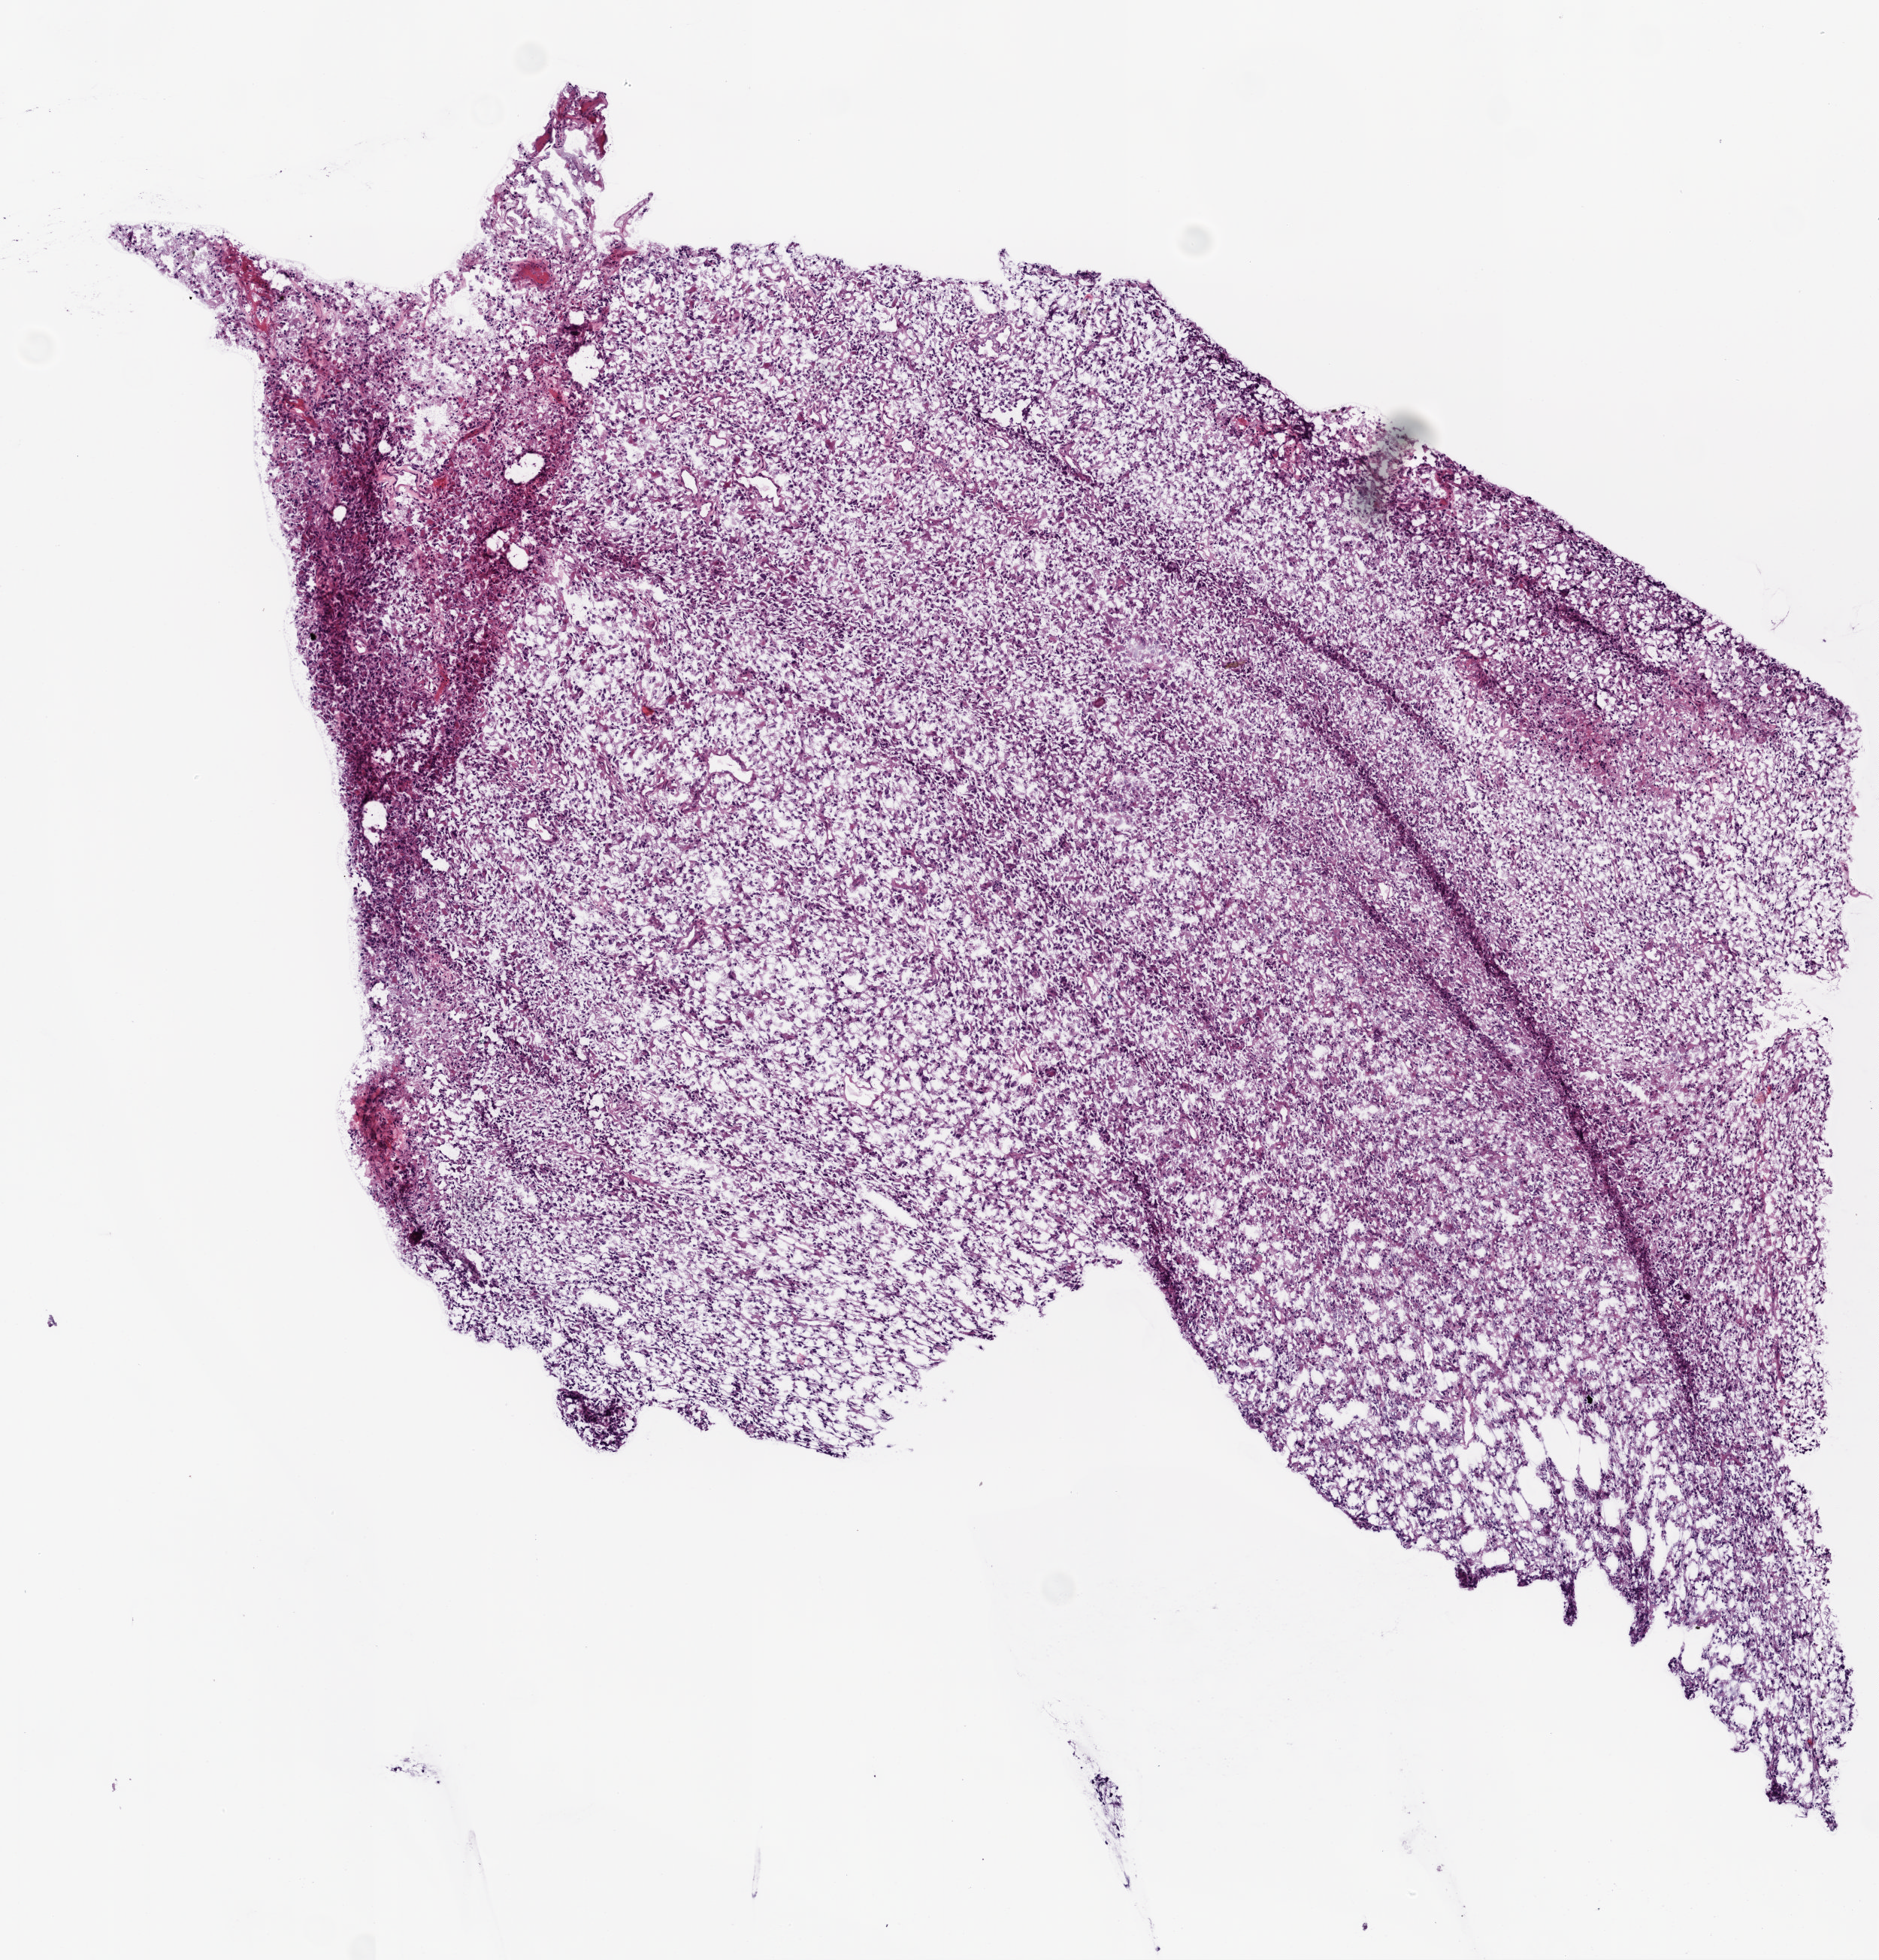
Whole-slide histology image, H&E-stained — a low-resolution overview of the entire scanned area, about 5.0 x 5.2 mm (slide scanned at 20x); frozen section from the top of the tissue portion; sample: primary tumour, brain. Female patient; age at initial diagnosis 77 years. Pathologist review of this section (percent, as recorded): tumour cells 90%, tumour nuclei 90%, normal cells 0%, stromal cells 5%, necrosis 5%.
- histologic diagnosis: Glioblastoma